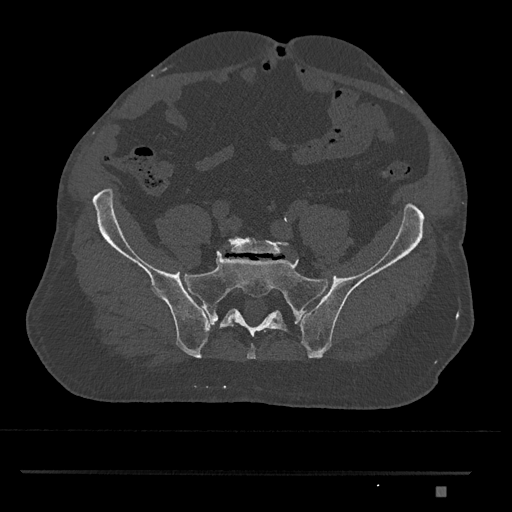
CT including the spine, one axial slice. Position 500 of 1134 along the scan axis. 120 kVp. Bone window (W 1800 / L 400 HU). 0.5 mm slice thickness. 512 × 512 image matrix, field of view 429 × 429 mm. Patient: male, 65 years. From the clinical record (not read from this slice): primary cancer: prostate.
Outlined on this slice (semi-automatic segmentation, software-assisted and operator-edited):
- L5 vertebra: bounding box [x1, y1, x2, y2] px = [227, 237, 289, 255]